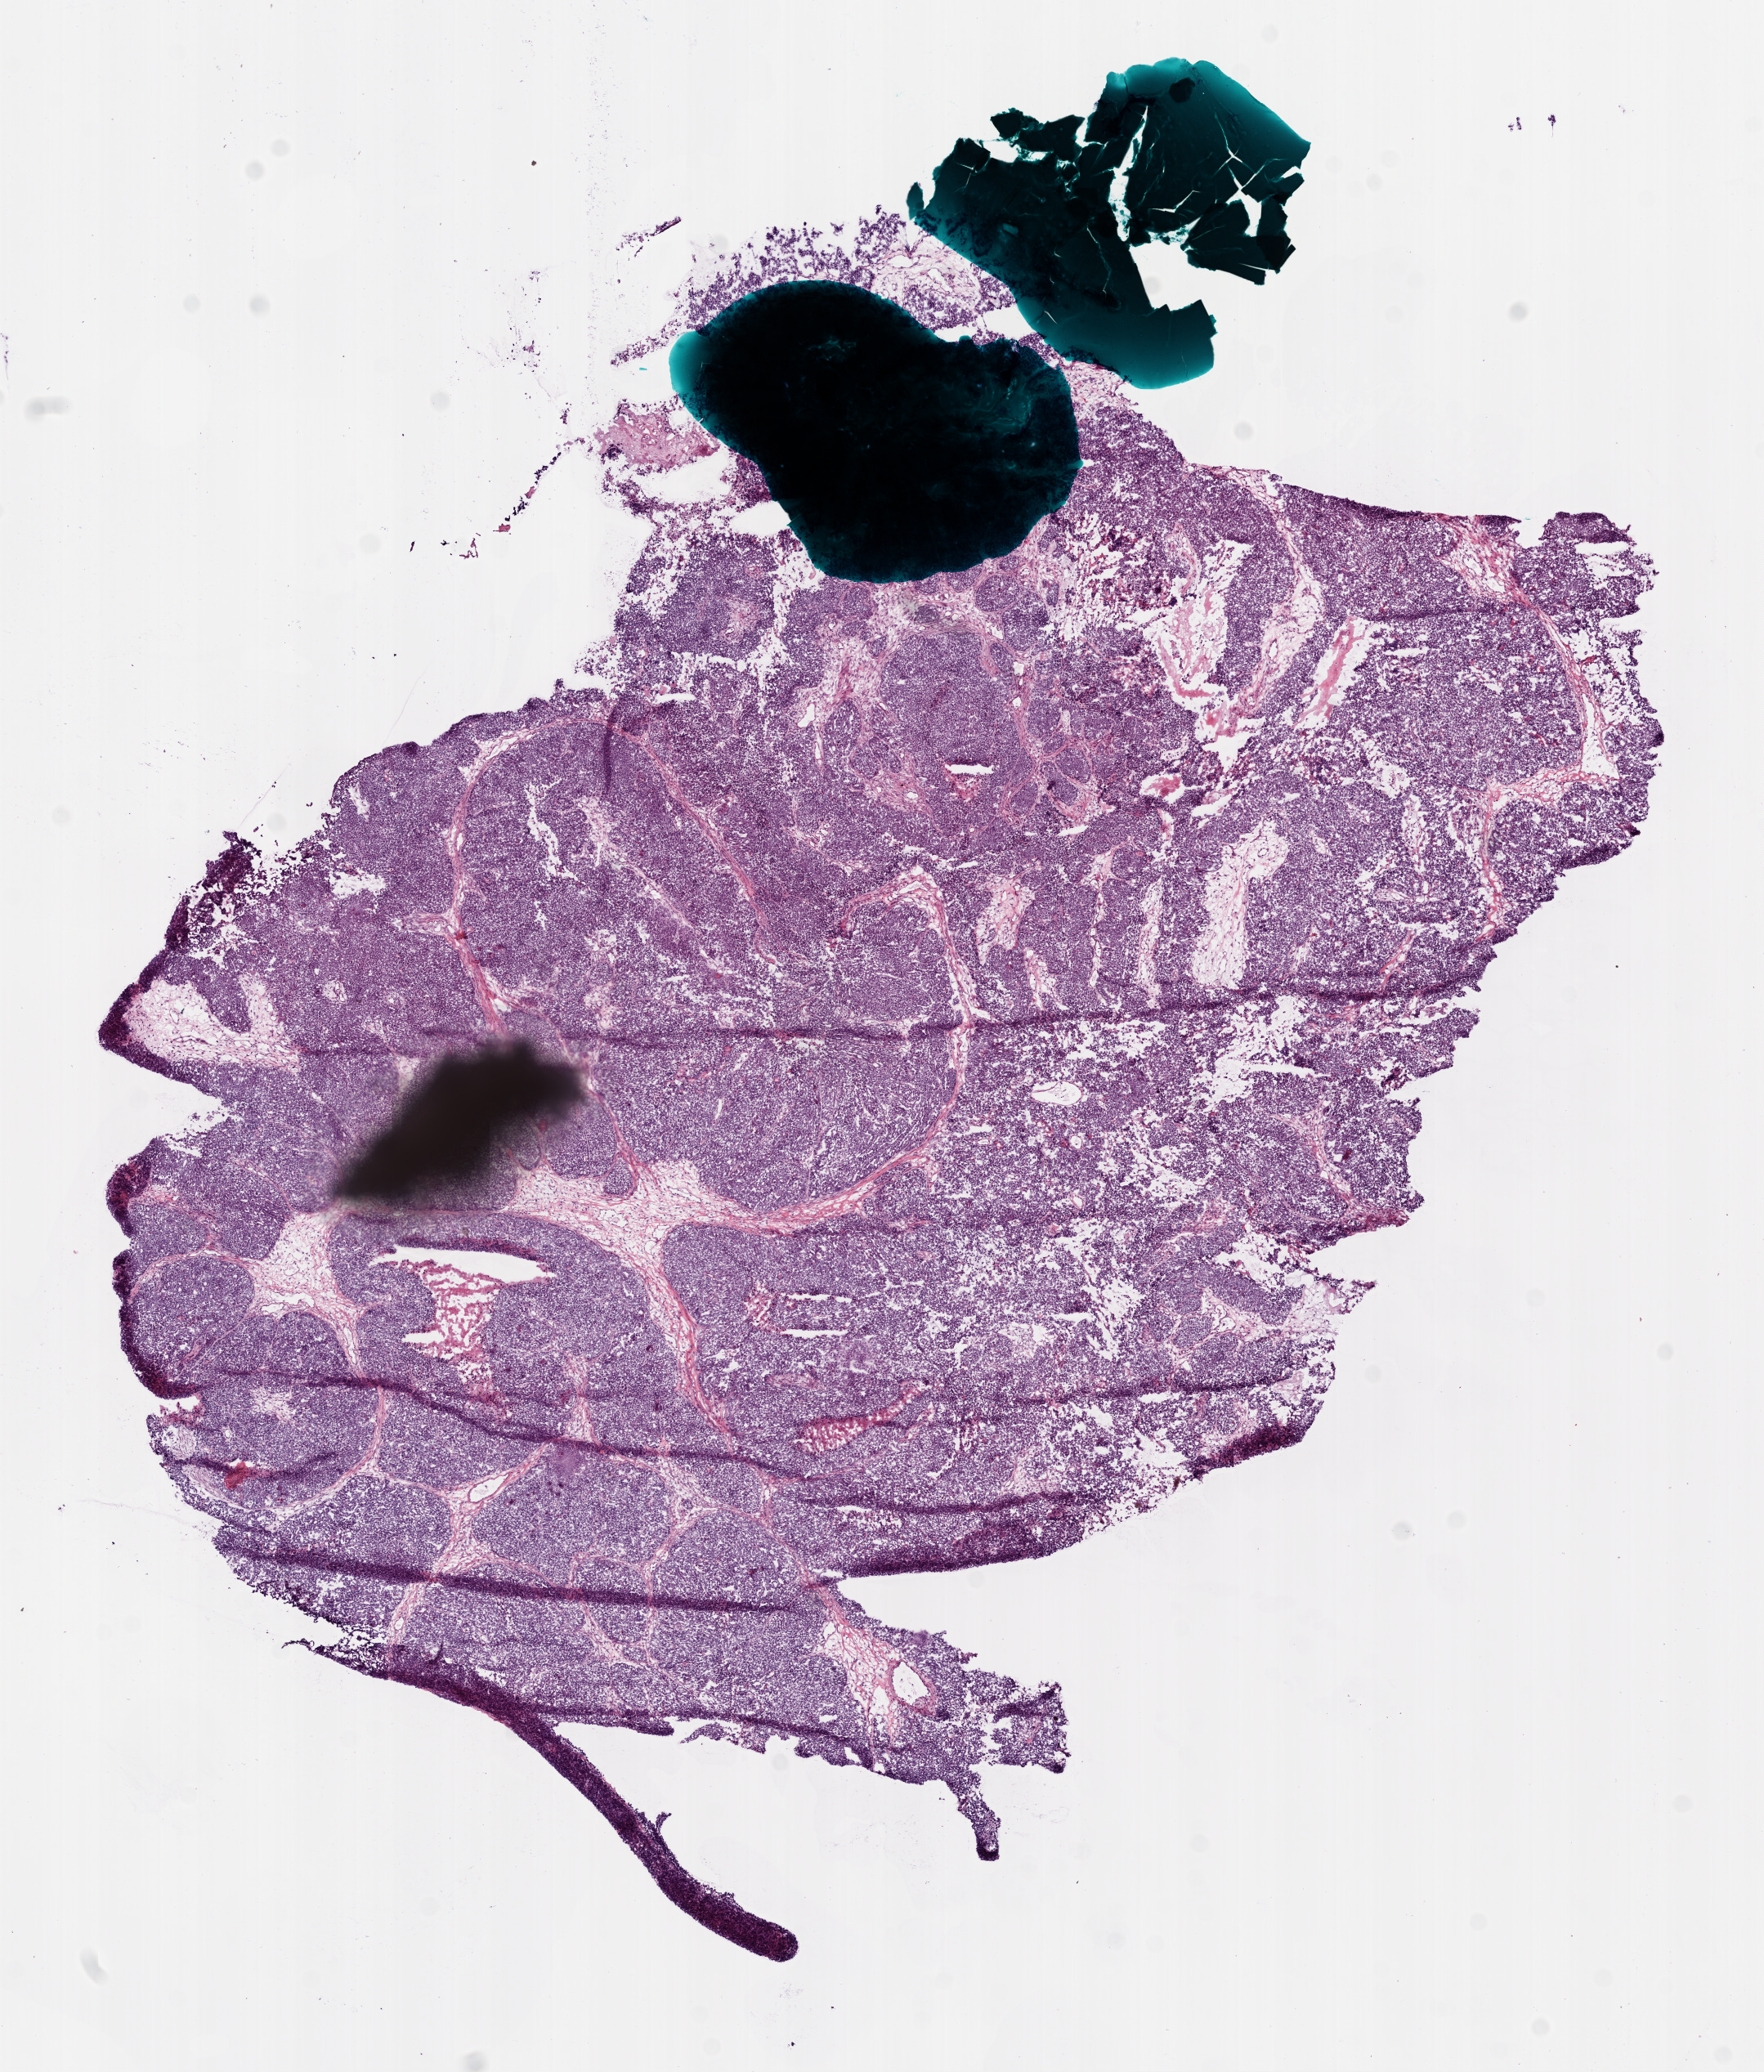
H&E-stained whole-slide image — a low-resolution overview of the entire scanned area, about 8.7 x 10.2 mm. Frozen section from the bottom of the tissue portion. Ovary, primary tumour sample. Patient: female, age at initial diagnosis 42 years. Histologic grade: G3 (poorly differentiated). Composition of this section per pathologist review: tumour nuclei 95%, normal cells 0%, necrosis 5%.
Histologic diagnosis: Serous cystadenocarcinoma, NOS. FIGO stage: IIIC.